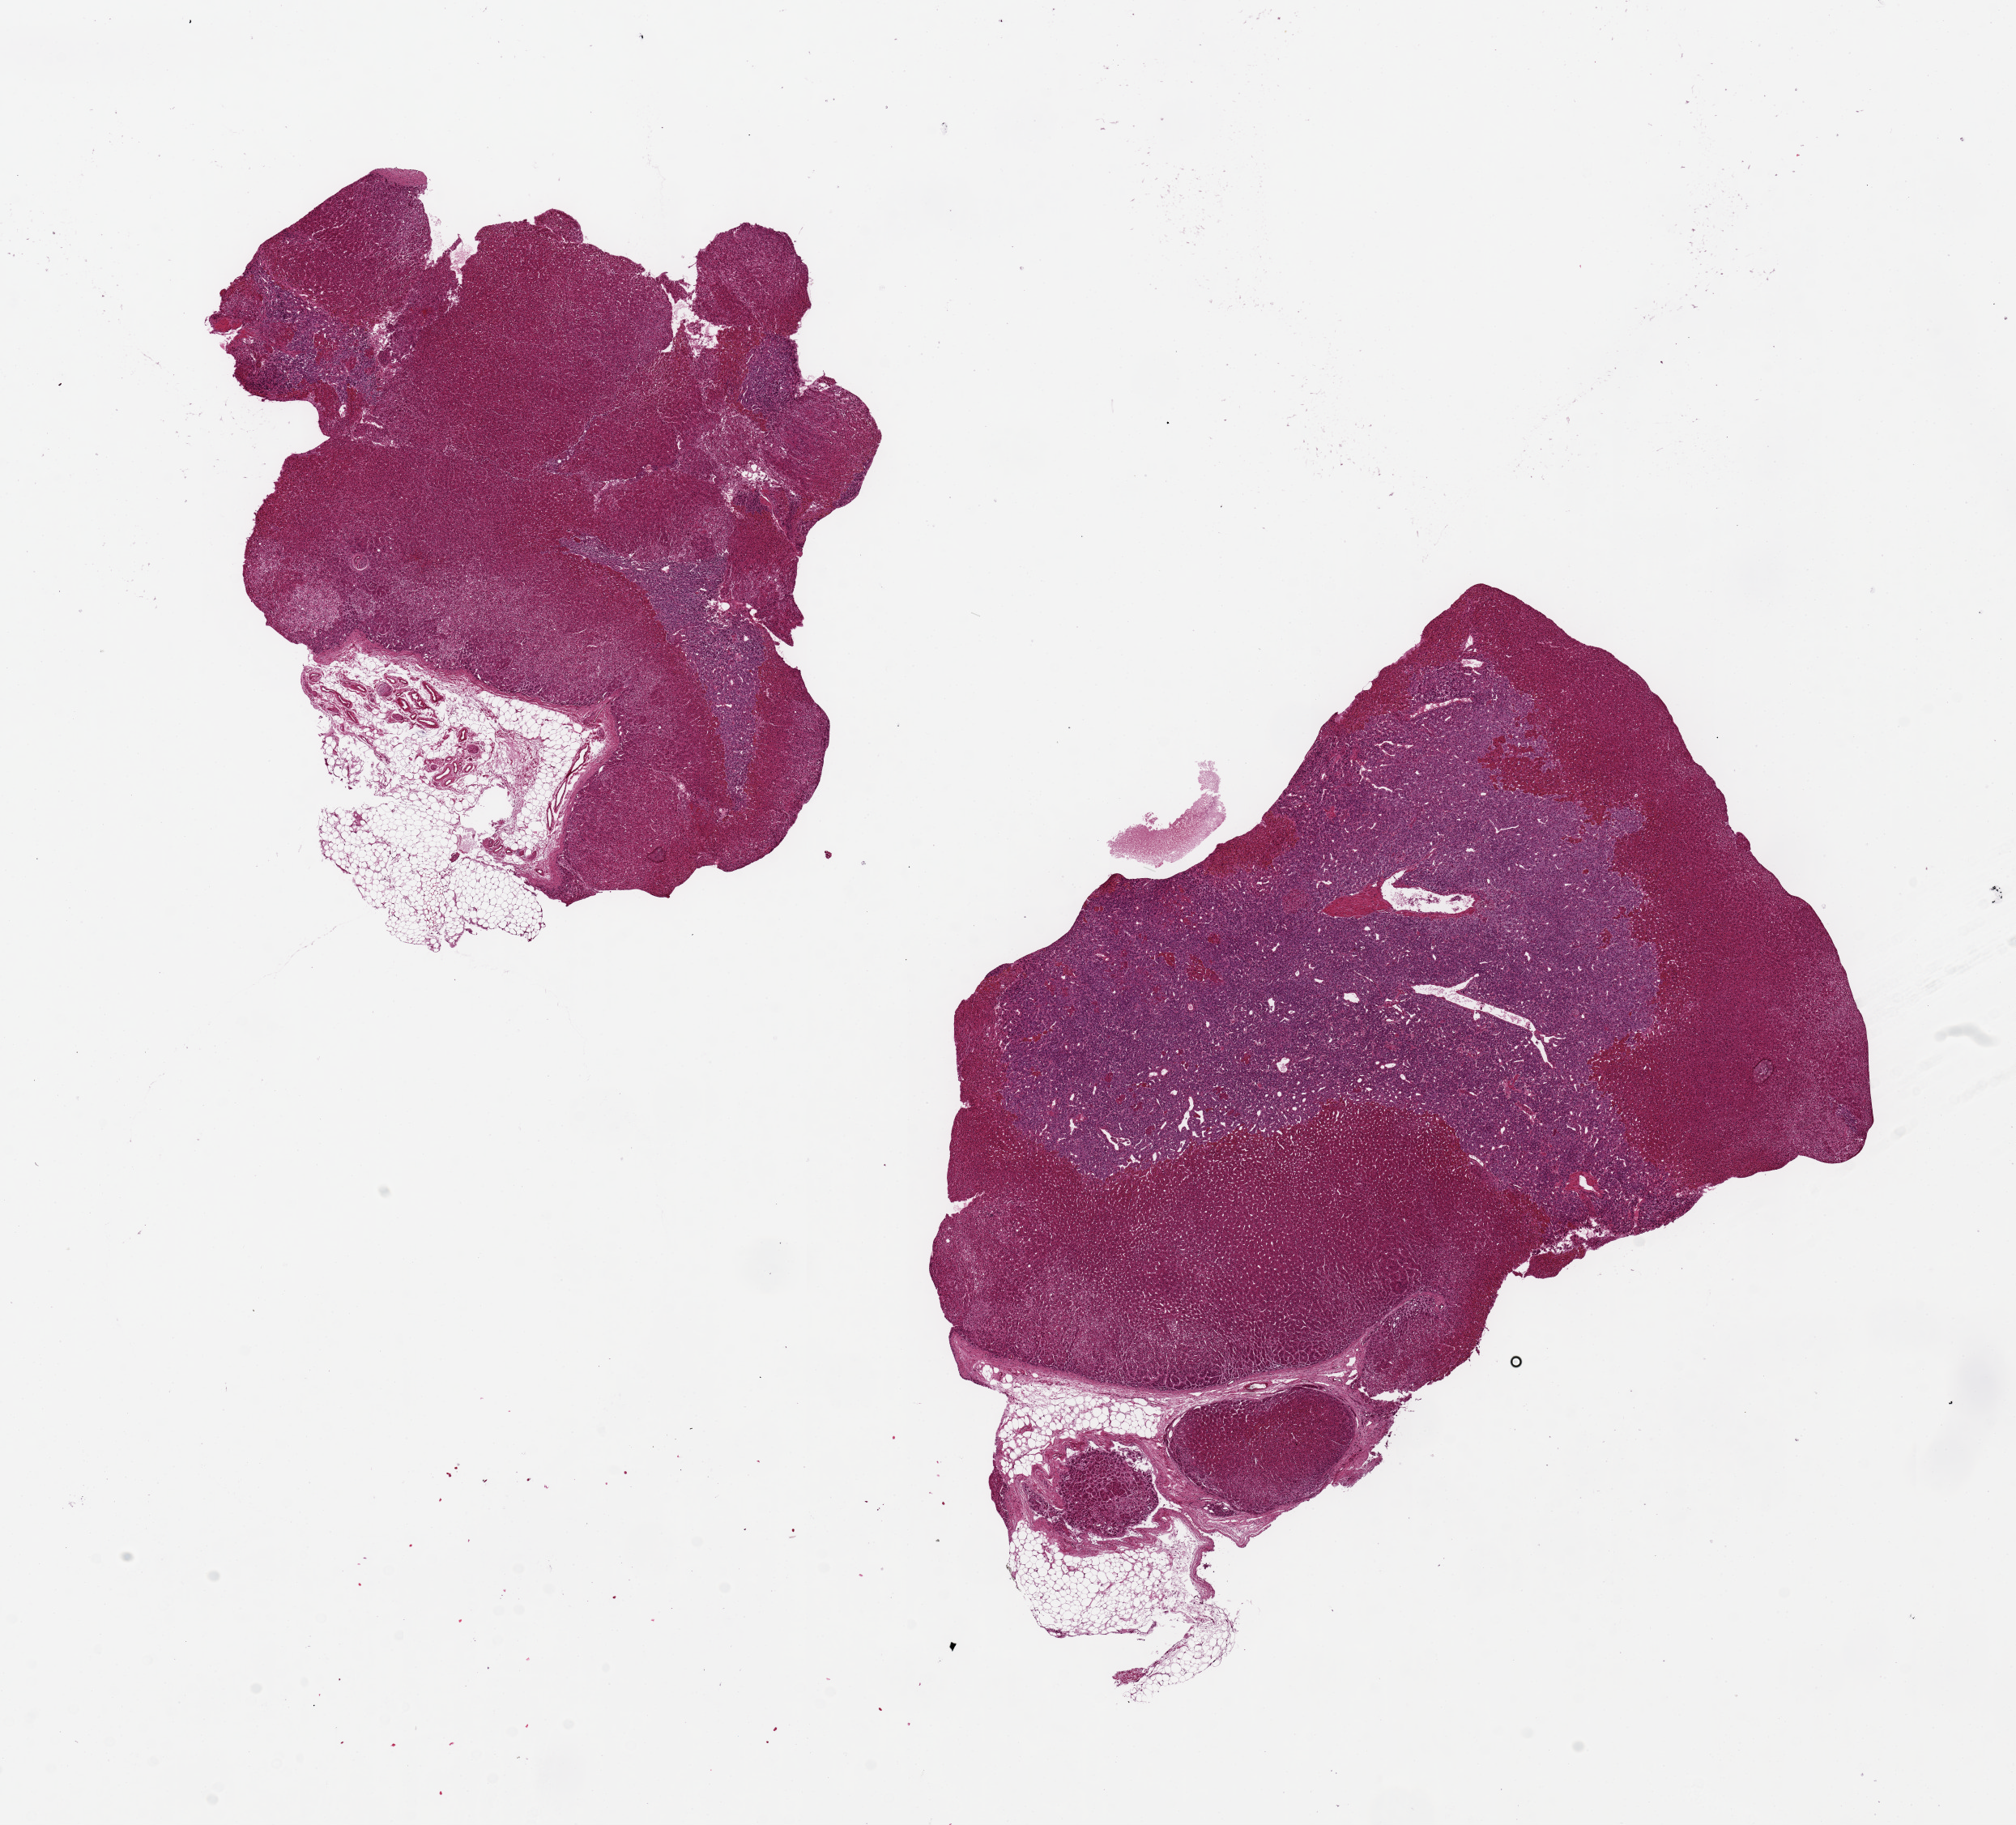
Whole-slide image, haematoxylin and eosin stain — whole scanned area (about 19.7 x 17.8 mm) shown as a low-resolution overview, PAXgene-fixed, paraffin-embedded tissue, target tissue: adrenal gland, donor tissue sample. Donor sex: male.
- review note (as recorded): 2 pieces, ~7x7mm. NOTE: unusually well-preserved with prominent medulla, also unusually well-preserved